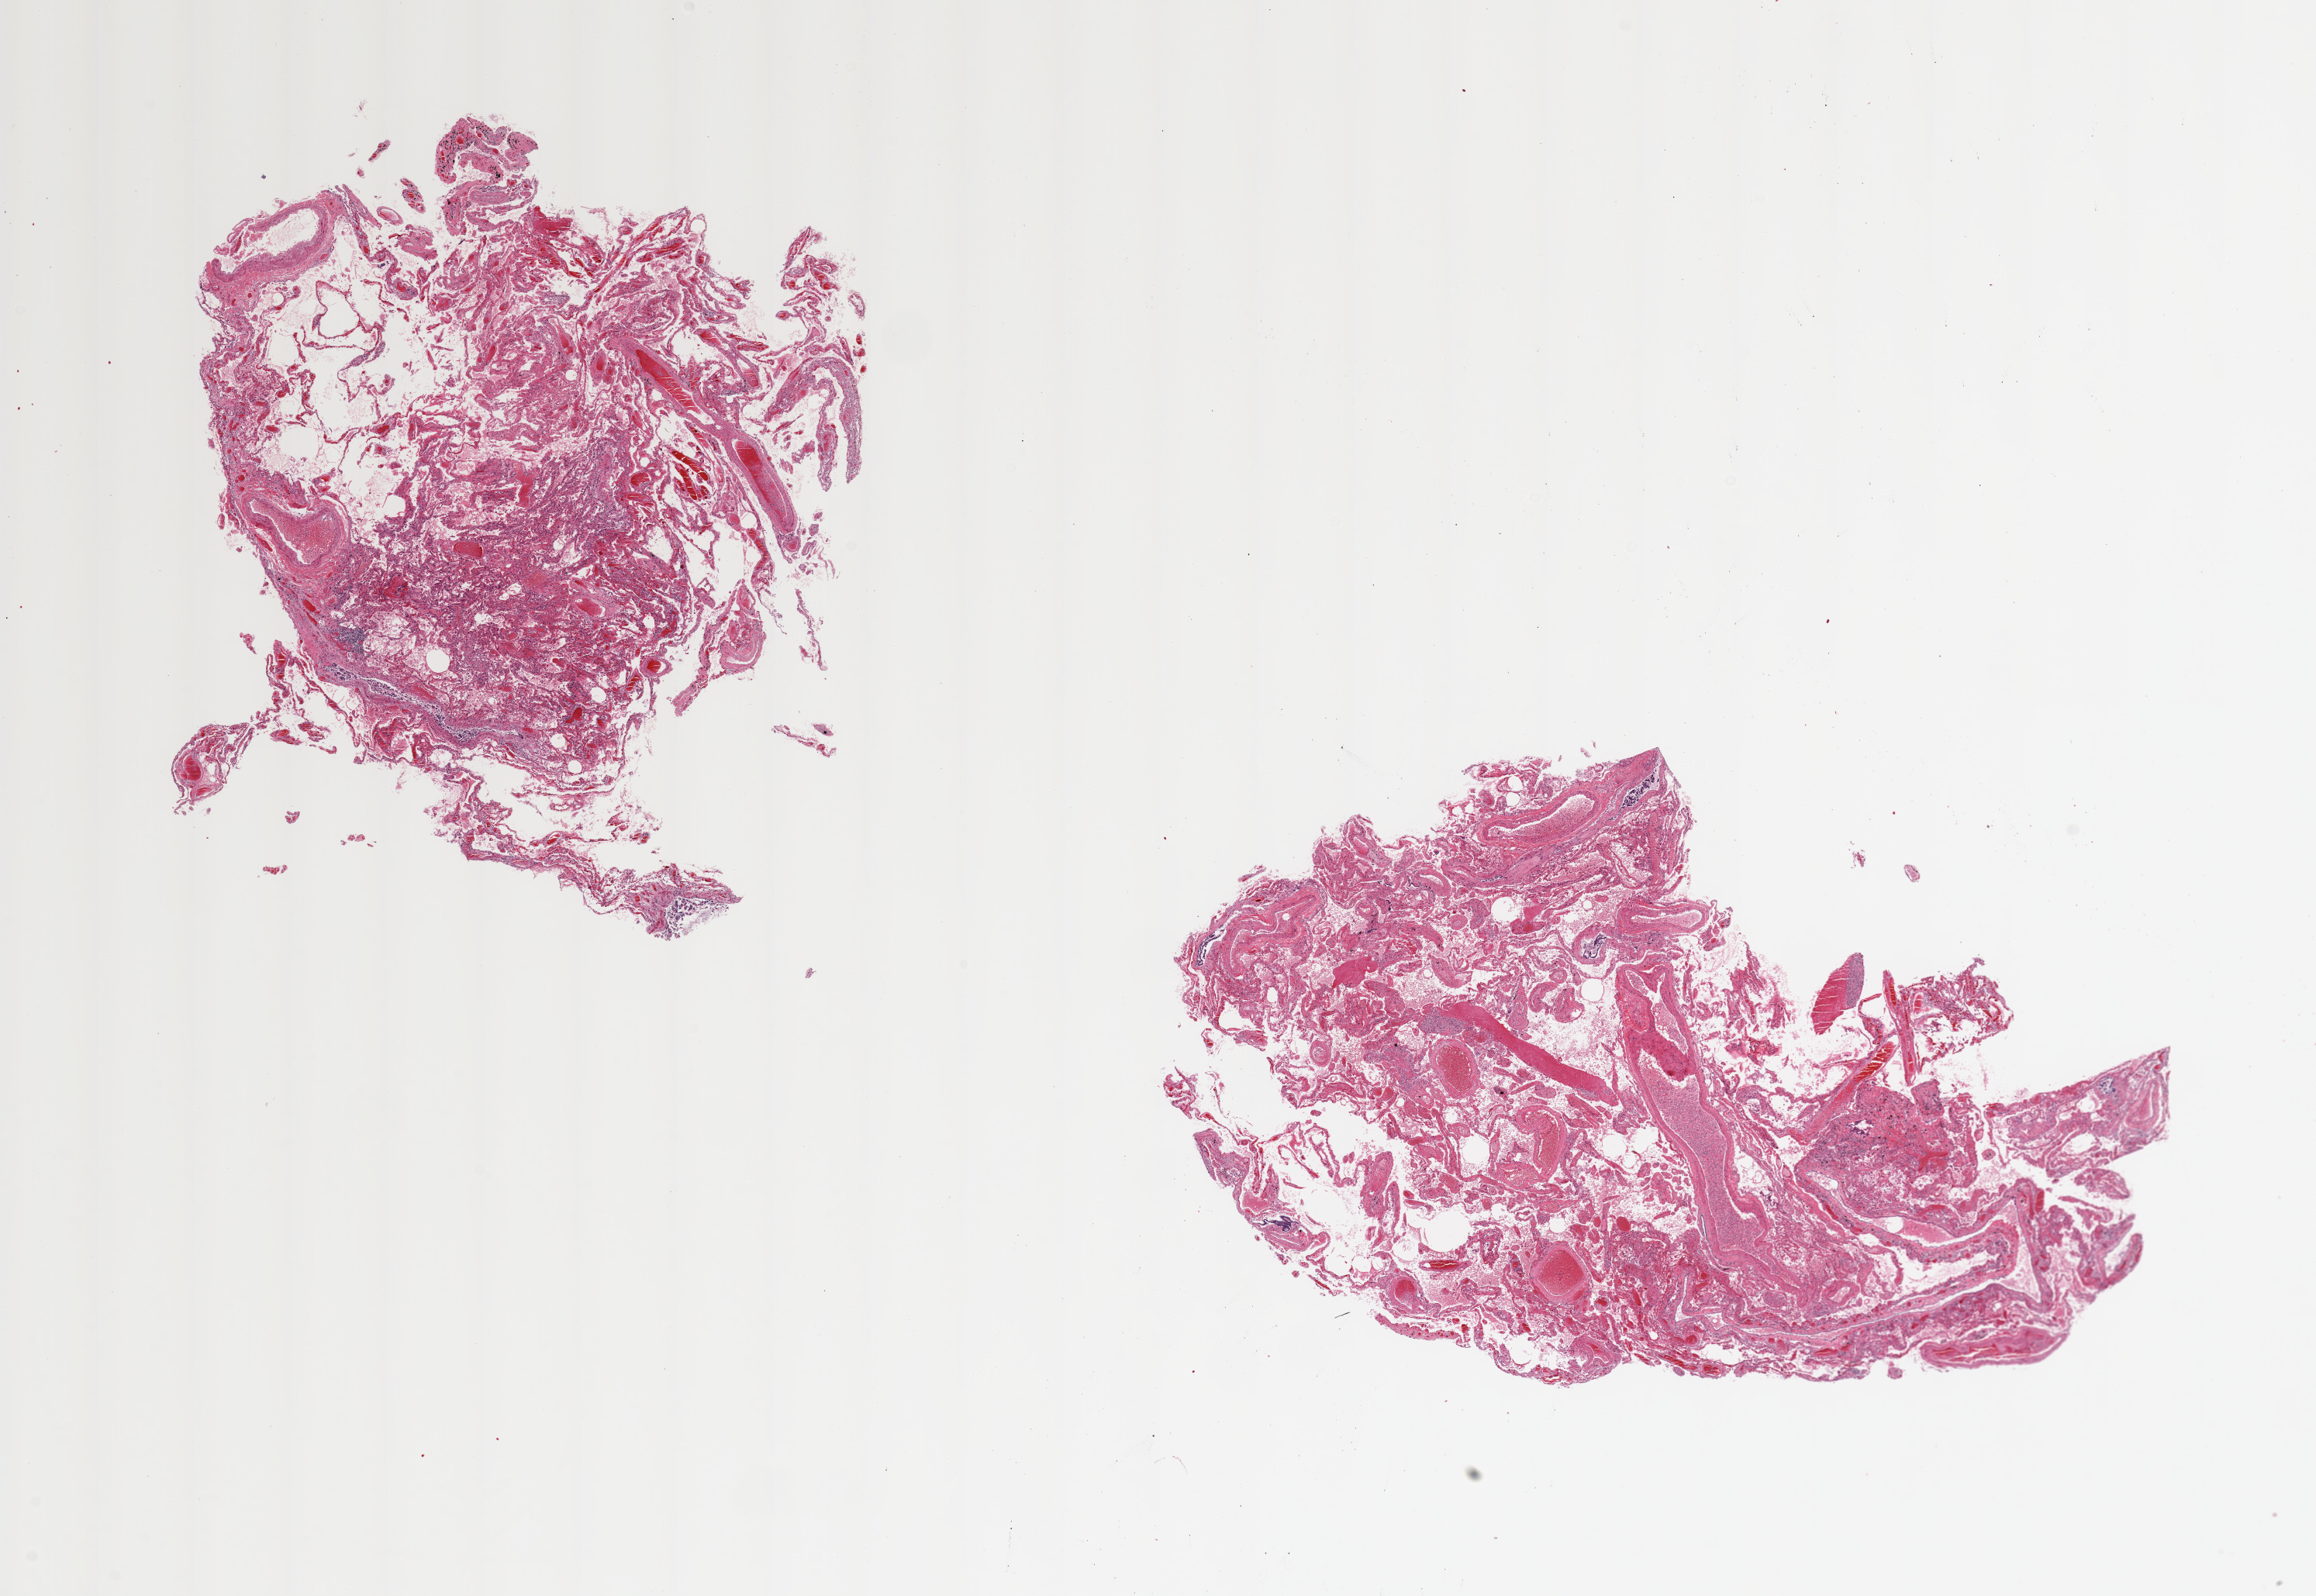
Digitized hematoxylin and eosin (H&E)-stained section — whole scanned area (about 23.6 x 16.3 mm, slide scanned at 20x) shown as a low-resolution overview; PAXgene-fixed, paraffin-embedded tissue; target tissue: lung; donor tissue sample. Donor: female.
• pathologist's review note for this sample: 2 pieces, 9x8.5 & 10x6.5mm; baadly autolyzed, diffuse active pneumonitis, possible diffuse alveolar damage sequence or other fibrosing pneumonitis, too autolyzed to evaluate further, consisten with clinical history